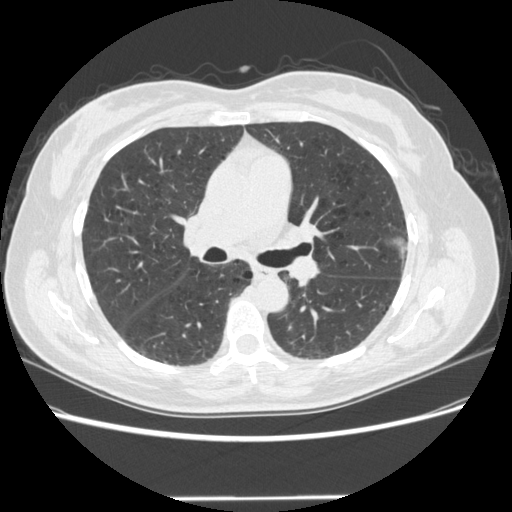
Axial slice from a low-dose chest CT screening exam; baseline annual screen; lung window (W 1500 / L -600 HU); standard (soft-tissue) reconstruction kernel (STANDARD). Female participant, aged 61 years at enrolment.
- Lesion marked by an expert reader, box from (x=383, y=227) to (x=428, y=277) px.
- Screening reader's record for this exam: no non-calcified nodule ≥4 mm recorded.
- Lung cancer was diagnosed 791 days after this screen (after the second annual screen): bronchiolo-alveolar adenocarcinoma, NOS, left upper lobe, well differentiated (G1), stage IA (AJCC 6th edition), 11 mm at pathology.